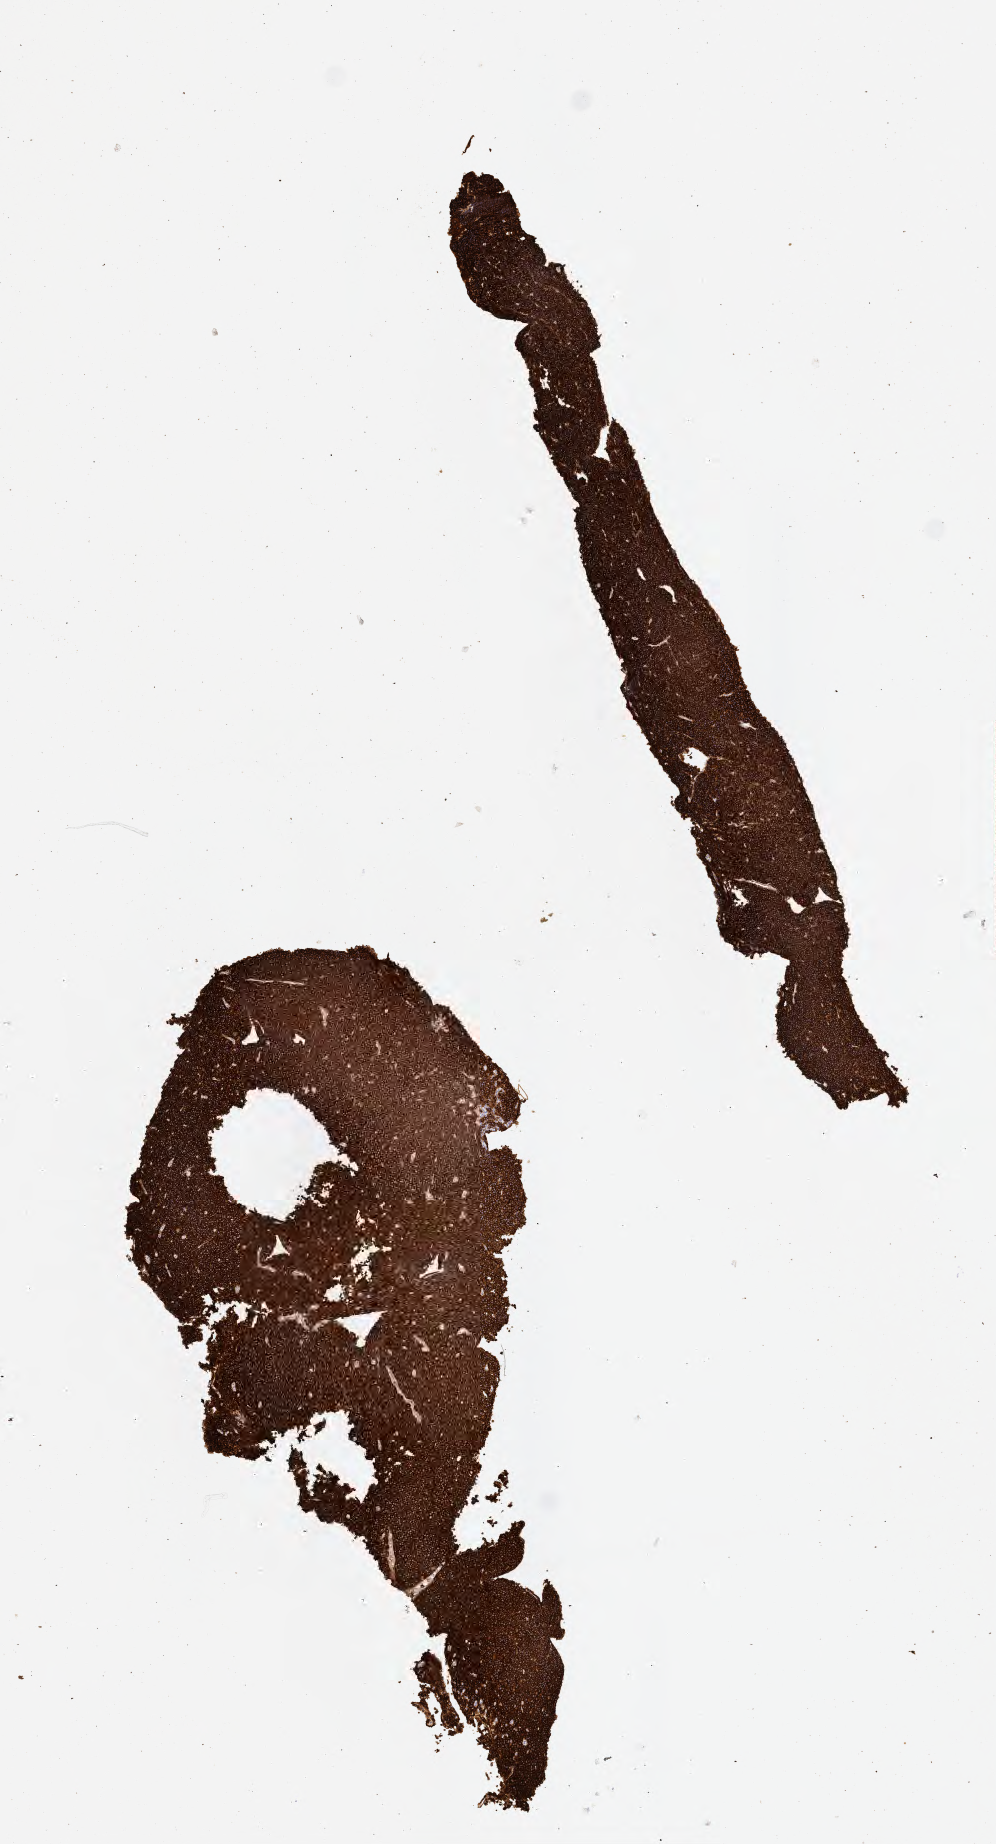
Immunohistochemistry (IHC) whole-slide image stained for CD20 — low-resolution overview of the scanned area, about 4.0 x 7.4 mm, specimen: tumor tissue. Patient: male, age at initial diagnosis 8 years.
• diagnosis: Burkitt lymphoma, NOS